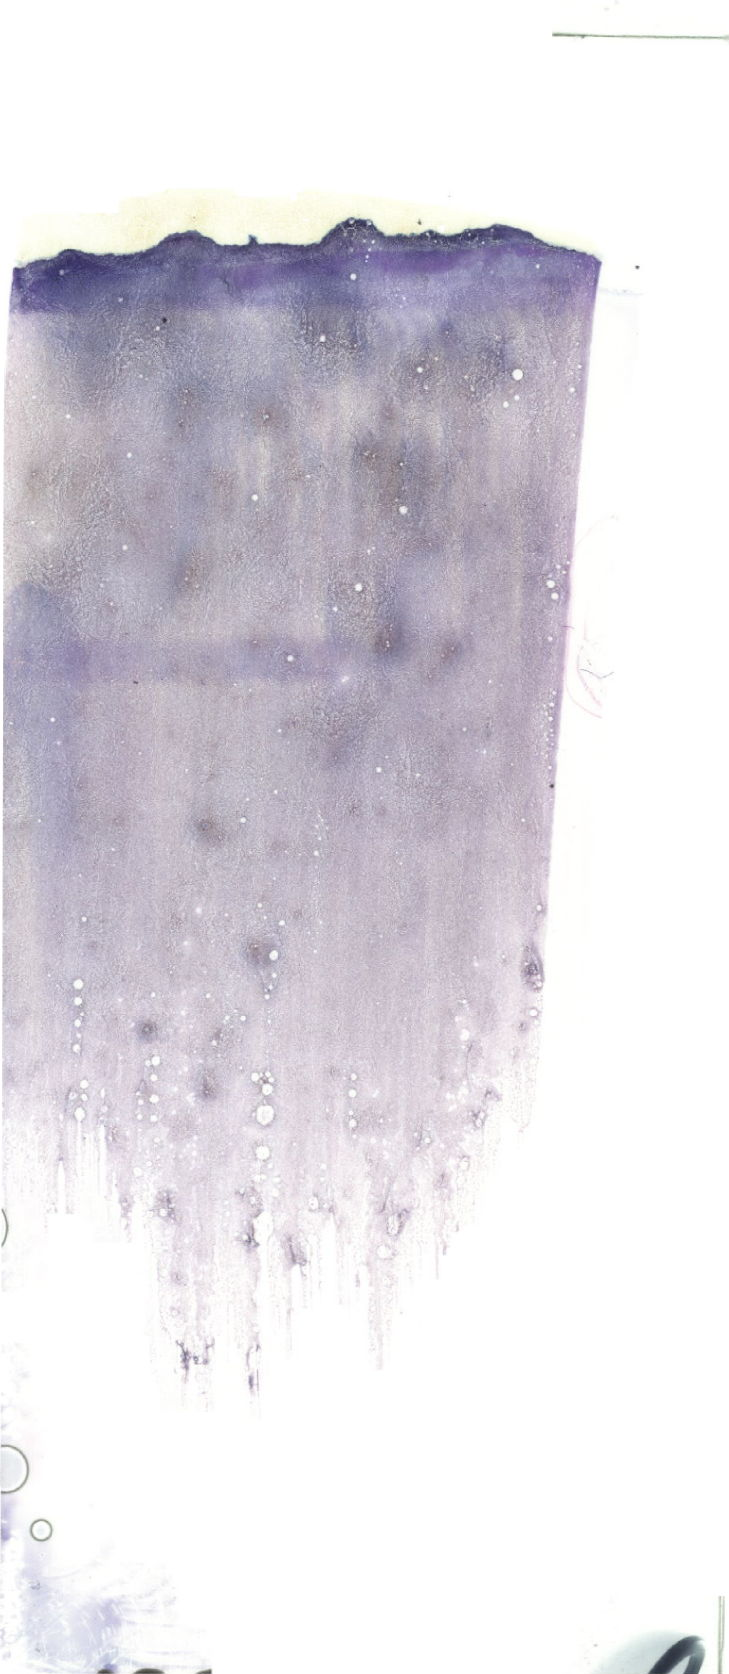
Whole-slide image of a May-Grünwald–Giemsa-stained bone marrow aspirate smear, shown as a low-resolution overview of the whole scanned area (about 20.7 x 47.4 mm). Patient sex: female.
• diagnosis: Acute Megakaryoblastic Leukemia